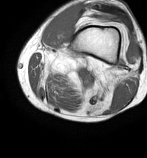
MRI of an extremity soft-tissue mass, one axial slice. MR volume resampled by the dataset authors to the PET/CT grid (not the native acquisition matrix). 147 × 158 image matrix, field of view 144 × 154 mm. Male patient. Case-level facts recorded for this patient, not image findings: histological type: undifferentiated pleomorphic liposarcoma; grade: high; site of the primary tumour: left thigh.
Annotated regions visible in this slice (expert contour drawn on MRI and transferred to this co-registered scan by the dataset authors):
- gross tumour volume including surrounding oedema: bounding box [x1, y1, x2, y2] px = [41, 63, 56, 84]